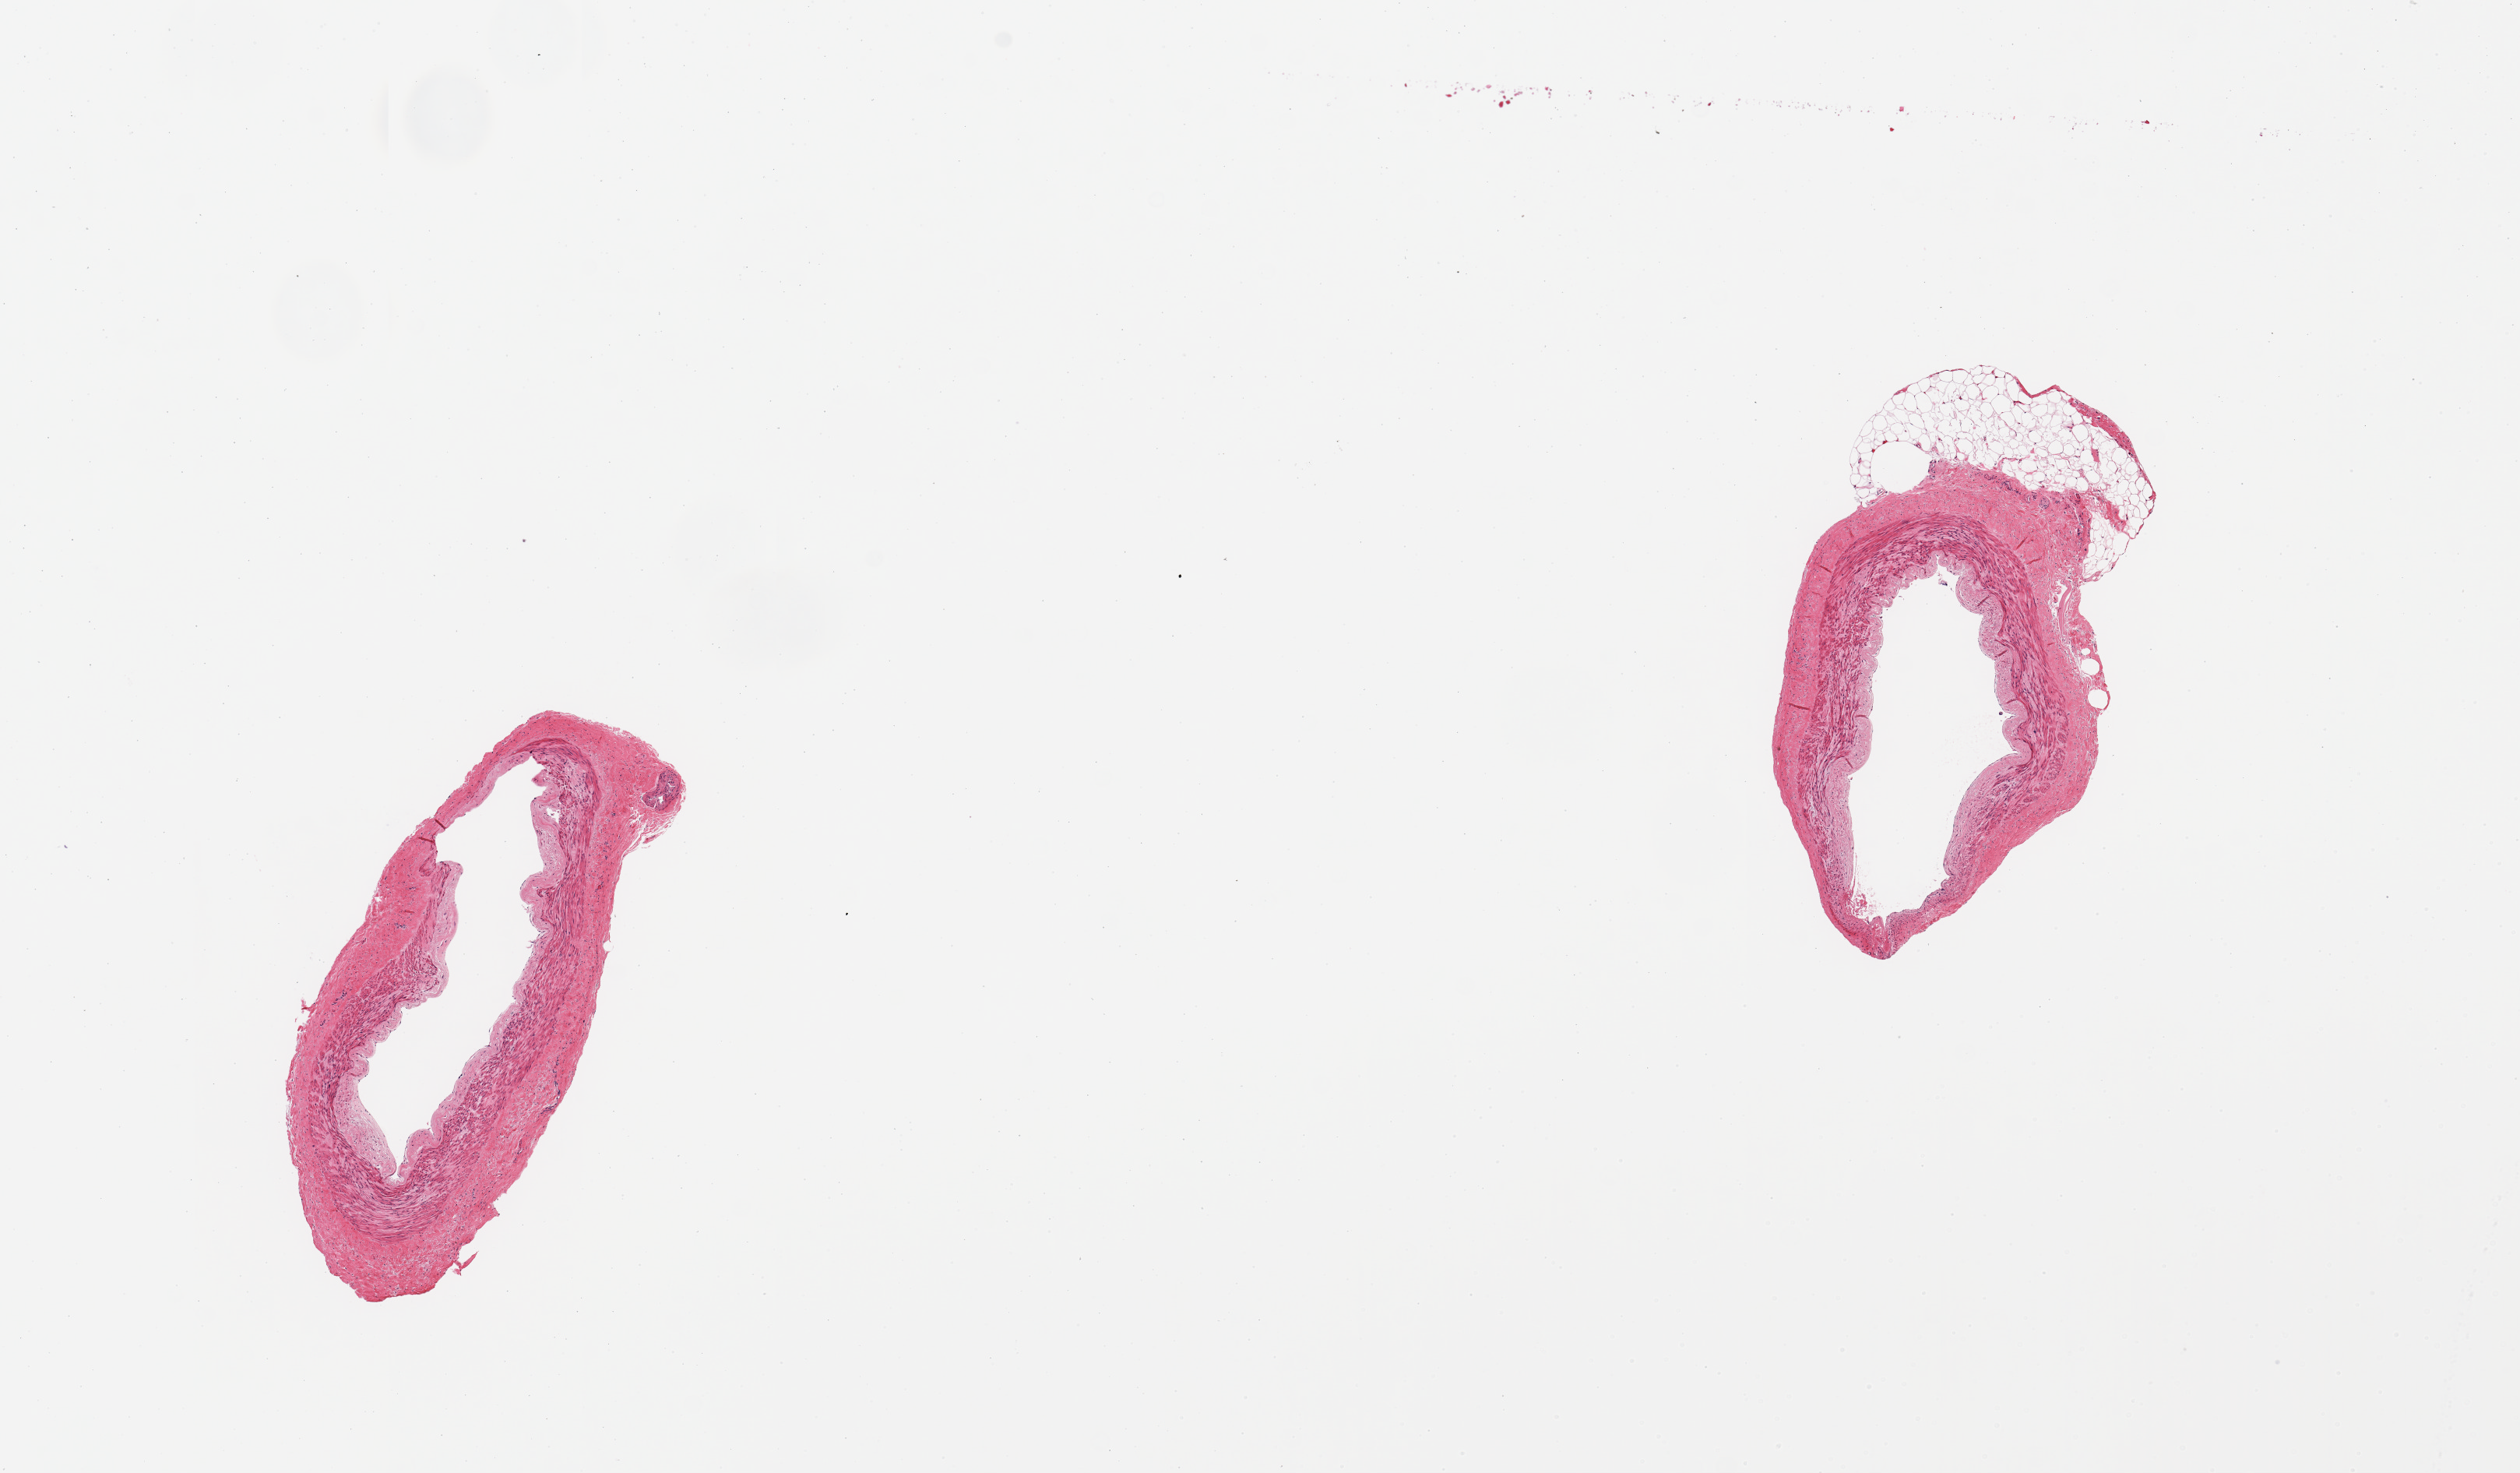
Digitized haematoxylin and eosin-stained section, brightfield — shown as a low-resolution overview of the whole scanned area (about 12.8 x 7.5 mm), PAXgene-fixed paraffin-embedded (PFPE) section, sampled site (target tissue): tibial artery, donor tissue sample.
Review note (as recorded): 2 pieces; well trimmed except for a 1.4 x 0.4mm external fat nodule.